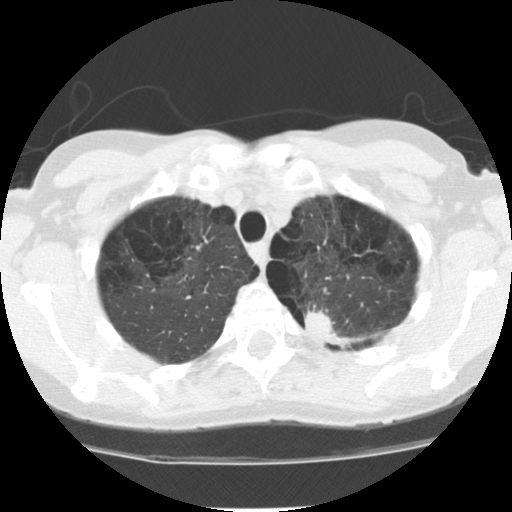
Low-dose screening chest CT, one axial slice; slice 97 of 116 in the series (ordered by position); reconstruction kernel STANDARD; 120 kVp; lung window (W 1500 / L -600 HU); 2.5 mm slice thickness; 512 × 512 image matrix, field of view 300 × 300 mm.
Structures marked on this image (manually delineated by an expert):
- lesion 1 (tumor, upper lobe of left lung): box from (x=304, y=310) to (x=345, y=343) px